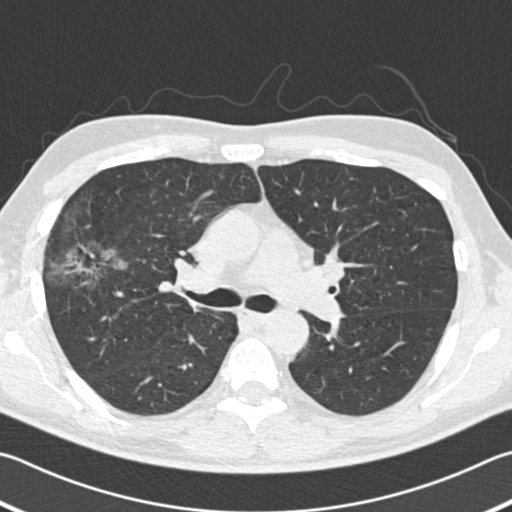
Axial slice from a low-dose chest CT screening exam, second screening round (one year after baseline), lung window (W 1500 / L -600 HU), standard (soft-tissue) reconstruction kernel (B30f), 120 kVp. Male participant, aged 56 years at enrolment. Former smoker at enrolment.
Lesion marked by an expert reader, bounding box <46,233,128,298> (left, top, right, bottom; pixels). Screening reader's record for this exam (one nodule recorded; not confirmed to be the boxed lesion): non-calcified nodule or mass ≥4 mm, right upper lobe, 18 × 14 mm, spiculated (stellate) margins, soft tissue attenuation, pre-existing on the prior screen: yes; interval growth: yes. Official screen result: positive, other. Participant outcome: lung cancer diagnosed 42 days after this screen — bronchiolo-alveolar adenocarcinoma, NOS, right upper lobe, well differentiated (G1), stage IIB (AJCC 6th edition), 30 mm at pathology.